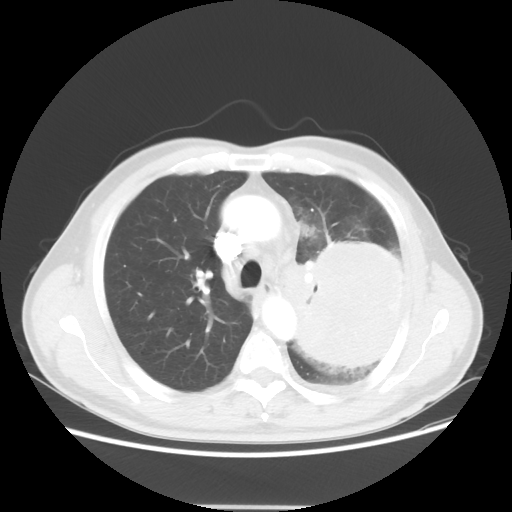
Chest CT, one axial slice; slice 37 of 53 in the series (ordered by position); 100 kVp; lung window (W 1500 / L -600 HU); 5 mm slice thickness; 512 × 512 image matrix, field of view 391 × 391 mm. Patient: male, 60 years. Case-level facts recorded for this patient, not image findings: clinical TNM (as recorded): T4 N1 M1a; histopathological grade: G3.
Outlined on this slice (bounding box drawn by a radiologist):
- lung tumour (recorded histology: large cell carcinoma): bounding box <284,235,415,384> (left, top, right, bottom; pixels)